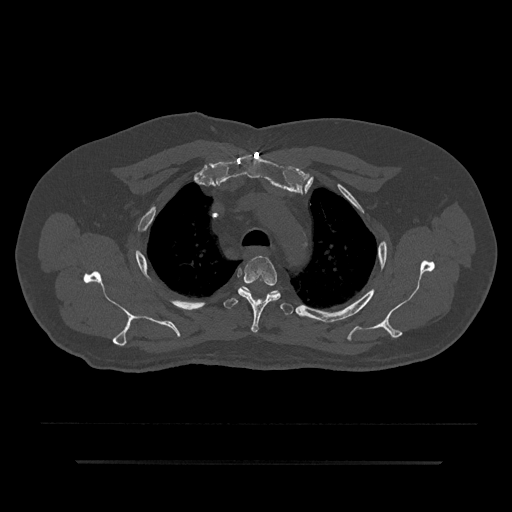
CT including the spine, one axial slice; slice 649 of 797 in the series (ordered by position); reconstruction kernel Br40s/3; 120 kVp; bone window (W 1800 / L 400 HU); 512 × 512 image matrix, field of view 464 × 464 mm. Male patient, age 59 years. From the clinical record (not read from this slice): primary cancer: bile ducts.
Annotated regions visible in this slice (semi-automatically segmented with operator editing):
- T3 vertebra: box from (x=238, y=256) to (x=281, y=333) px
- T4 vertebra: (x=223, y=288)–(x=294, y=315)